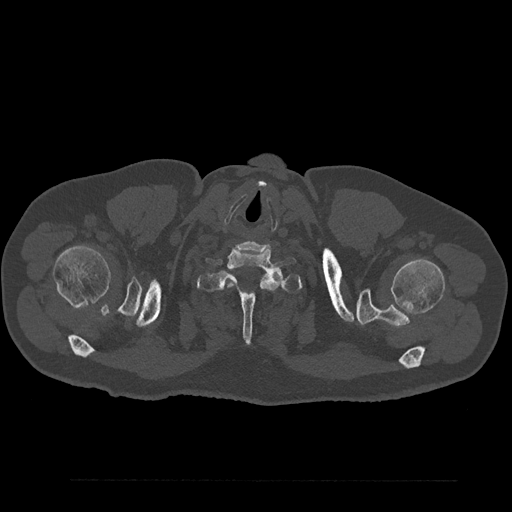
CT including the spine, one axial slice. Slice 767 of 797 in the series (ordered by position). Reconstruction kernel Br40s/3. 120 kVp. Bone window (W 1800 / L 400 HU). 0.5 mm slice thickness. 512 × 512 image matrix, field of view 430 × 430 mm. Patient: male, 61 years. From the clinical record (not read from this slice): primary cancer: prostate.
Structures marked on this image (semi-automatic segmentation, software-assisted and operator-edited):
- T1 vertebra: bounding box [x1, y1, x2, y2] px = [197, 261, 303, 344]